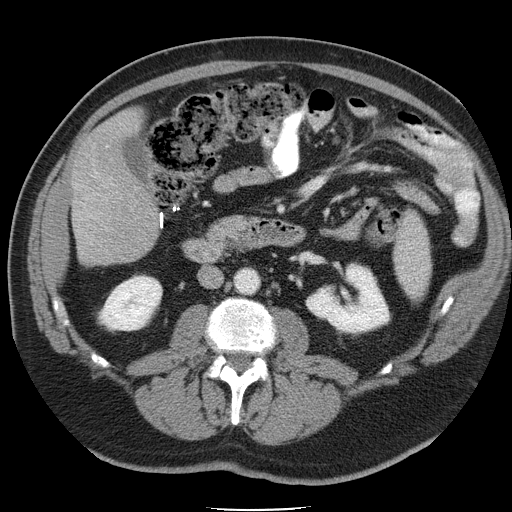
Contrast-enhanced abdominal CT, one axial slice; slice 13 of 45 in the series (ordered by position); 120 kVp; intravenous contrast given; soft-tissue window (W 400 / L 40 HU); 512 × 512 image matrix. Male patient, age 65 years. From the clinical record (not read from this slice): diagnosis: colorectal cancer liver metastases, imaged before liver resection; multiple liver metastases: yes; largest metastasis: 4.9 cm; disease in both lobes: no.
Annotated regions visible in this slice (expert manual segmentation):
- liver: bounding box <72,113,159,265> (left, top, right, bottom; pixels)
- planned liver remnant (the part of the liver to remain after resection): <95,114,138,155>